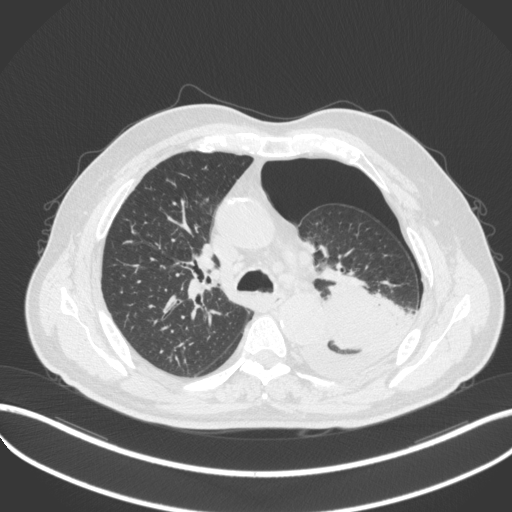
Chest CT, one axial slice. Position 343 of 466 along the scan axis. 120 kVp. Lung window (W 1500 / L -600 HU). 1 mm slice thickness. 512 × 512 image matrix, field of view 400 × 400 mm. Male patient, age 76 years. Case-level facts recorded for this patient, not image findings: clinical TNM (as recorded): T3 N0 M1b.
Structures marked on this image (rectangle marked by the reading radiologist):
- lung tumour (recorded histology: adenocarcinoma): bounding box (x1, y1, x2, y2) in pixels: (302, 275, 419, 385)